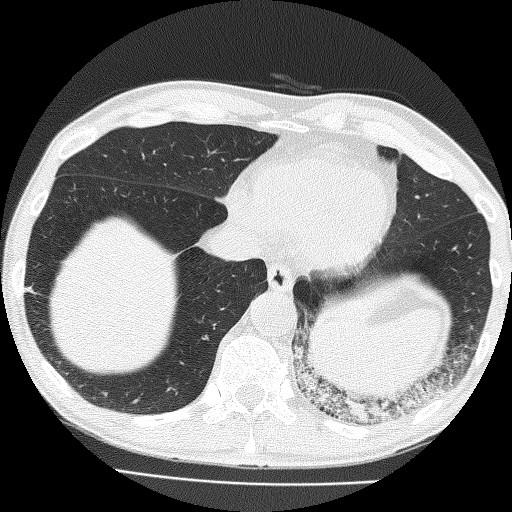
Low-dose screening chest CT, one axial slice. Position 46 of 160 along the scan axis. Reconstruction kernel FC51. 120 kVp. Lung window (W 1500 / L -600 HU). 2 mm slice thickness. 512 × 512 image matrix, field of view 324 × 324 mm.
Annotated regions visible in this slice (expert manual segmentation):
- lesion 1 (tumor, lower lobe of left lung): box from (x=341, y=397) to (x=373, y=421) px